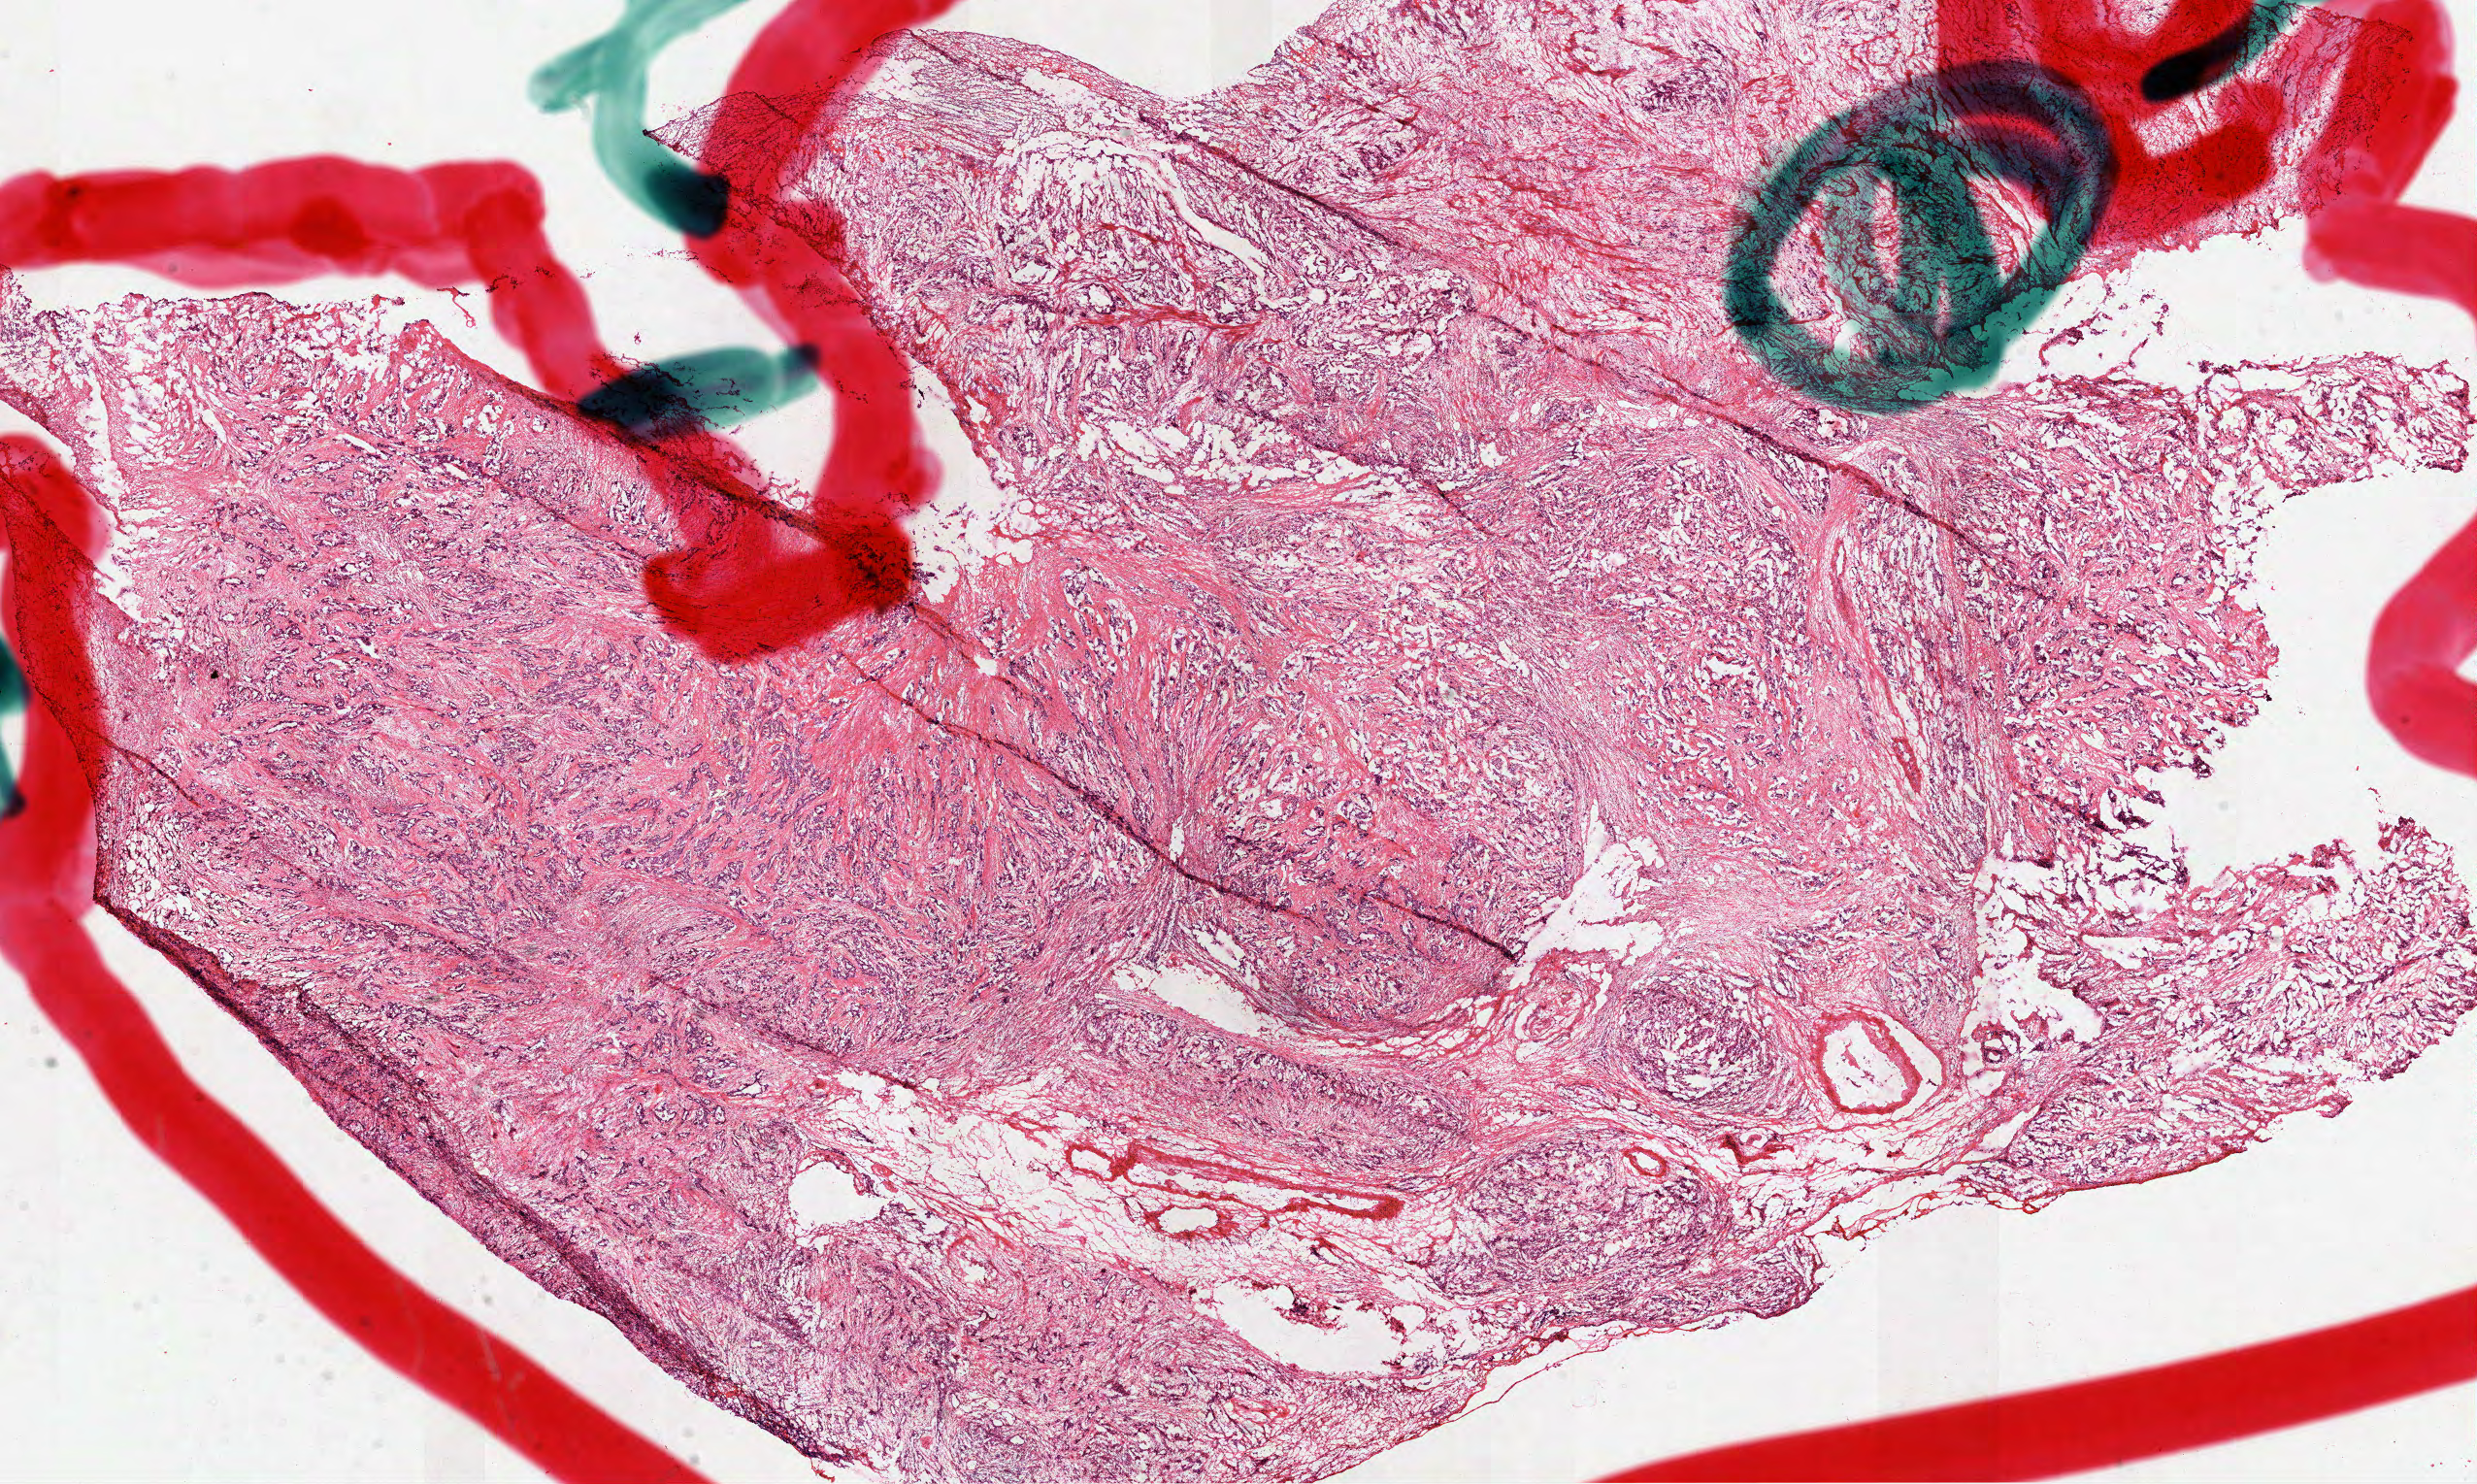
Whole-slide histology image, H&E, a low-resolution overview of the entire scanned area, about 20.6 x 12.3 mm (acquisition: 40x scan). Frozen section. Stomach, primary tumour sample. Patient: female, age at initial diagnosis 57 years.
Diagnosis: Adenocarcinoma, NOS (body of stomach).